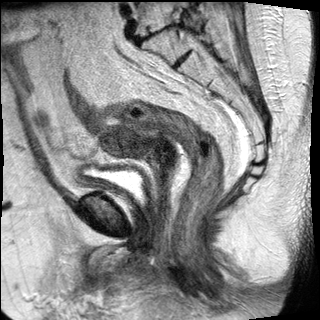
Pelvic MRI for cervical cancer, one sagittal slice. Slice 14 of 27 in the series (ordered by position). T2-weighted. 1.5 T. TE 89 ms, TR 2740 ms. 320 × 320 image matrix. Patient: female, 67 years.
Outlined on this slice (outlined manually by an expert reader):
- uterus and cervix: bounding box [x1, y1, x2, y2] px = [100, 124, 181, 175]